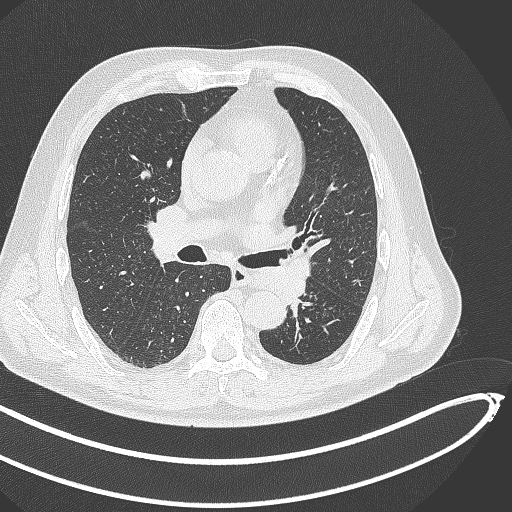
Chest CT, one axial slice; reconstruction kernel B70f; lung window (W 1500 / L -600 HU); 1 mm slice thickness; 512 × 512 image matrix, field of view 400 × 400 mm. Patient: male, 64 years. Case-level facts recorded for this patient, not image findings: clinical TNM (as recorded): T1c N0 M0; histopathological grade: G2.
Annotated regions visible in this slice (bounding box drawn by a radiologist):
- lung tumour (recorded histology: squamous cell carcinoma): box from (x=252, y=255) to (x=313, y=301) px